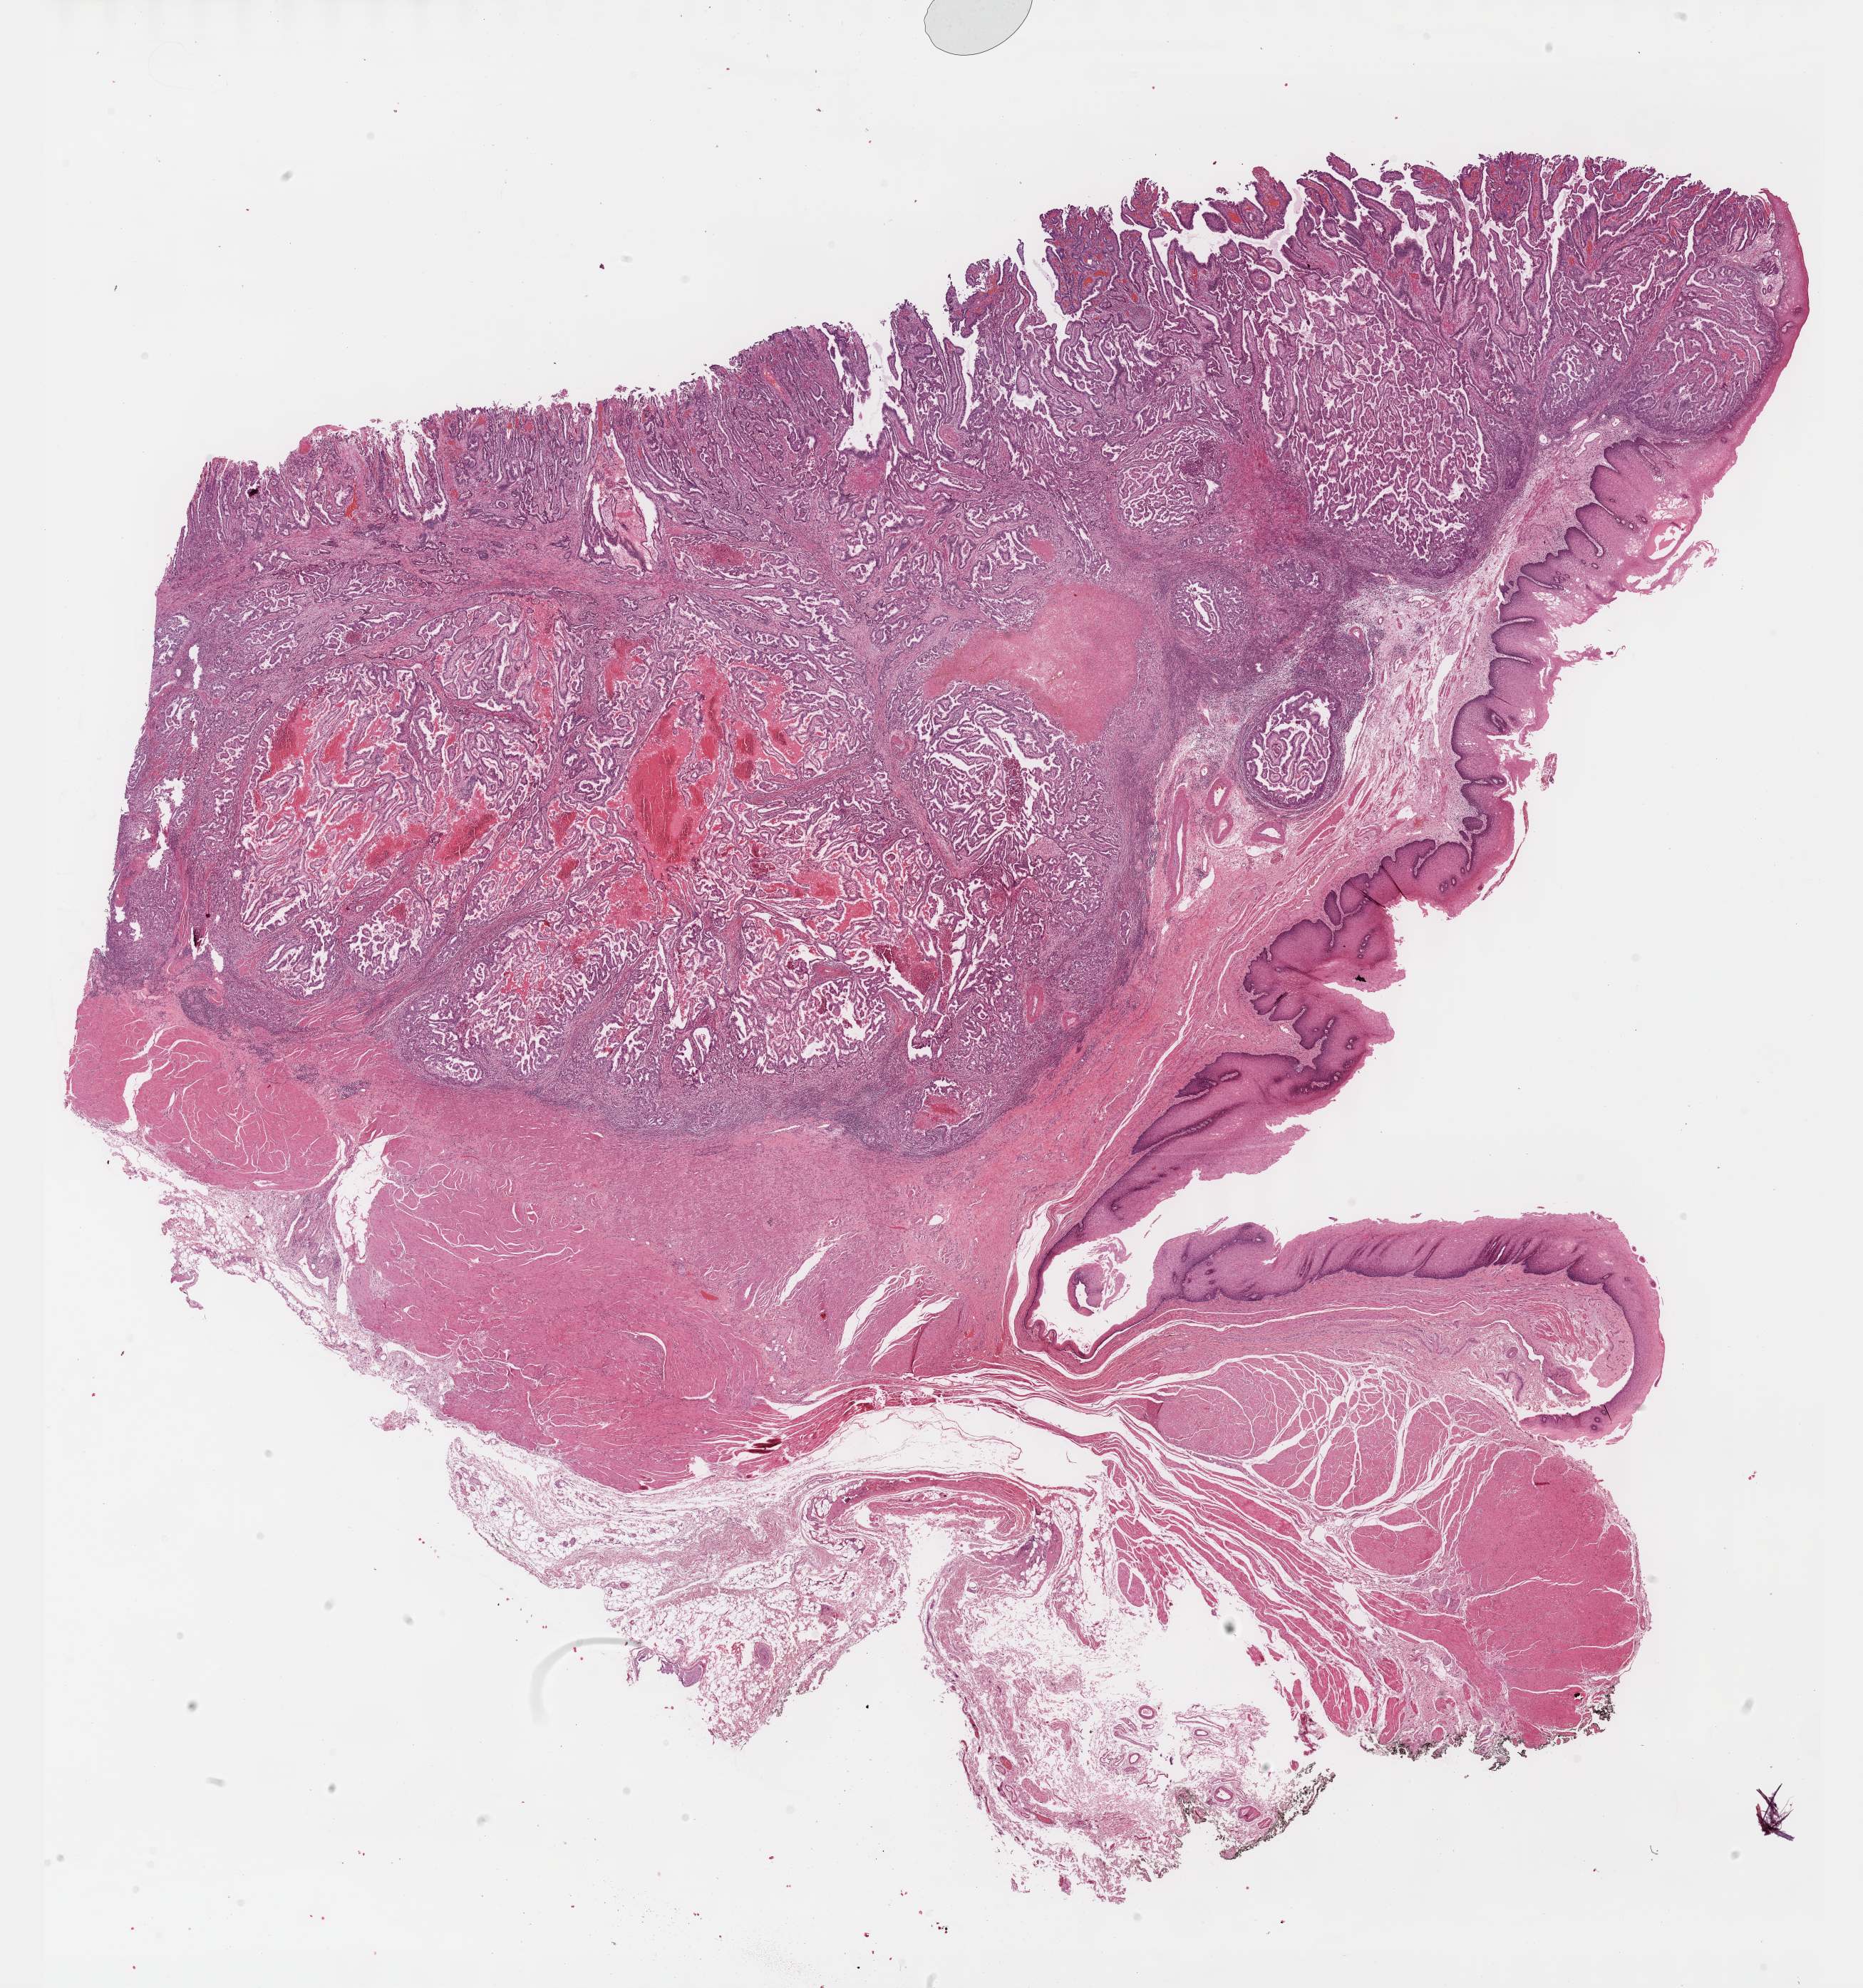
Digitized H&E tissue section (whole slide) — a low-resolution overview of the entire scanned area, about 21.1 x 22.5 mm. FFPE section. Primary tumour sample from the stomach. Male, age 78 years at initial diagnosis. Histologic grade: G3 (poorly differentiated).
Diagnosis: Tubular adenocarcinoma. AJCC pathologic stage: IIIB (7th edition).